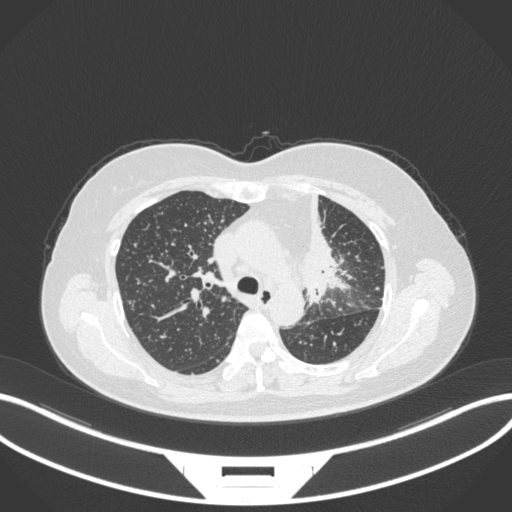
Chest CT, one axial slice; reconstruction kernel B31f; lung window (W 1500 / L -600 HU); 1 mm slice thickness; 512 × 512 image matrix, field of view 400 × 400 mm. Female patient, age 49 years. From the clinical record (not read from this slice): clinical TNM (as recorded): T1c N0 M1.
Structures marked on this image (bounding box drawn by a radiologist):
- lung tumour (recorded histology: adenocarcinoma): bounding box (x1, y1, x2, y2) in pixels: (298, 190, 348, 304)